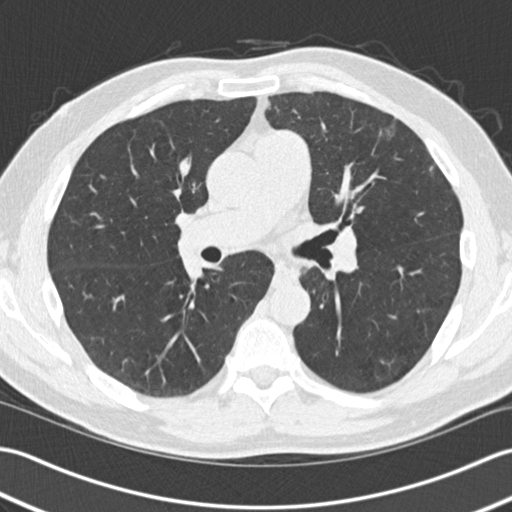
Low-dose screening chest CT, one axial slice. Slice 72 of 140 in the series (ordered by position). Reconstruction kernel B30f. Lung window (W 1500 / L -600 HU). 512 × 512 image matrix.
Annotated regions visible in this slice (expert manual segmentation):
- lesion 1 (tumor, upper lobe of left lung): box from (x=430, y=166) to (x=433, y=171) px